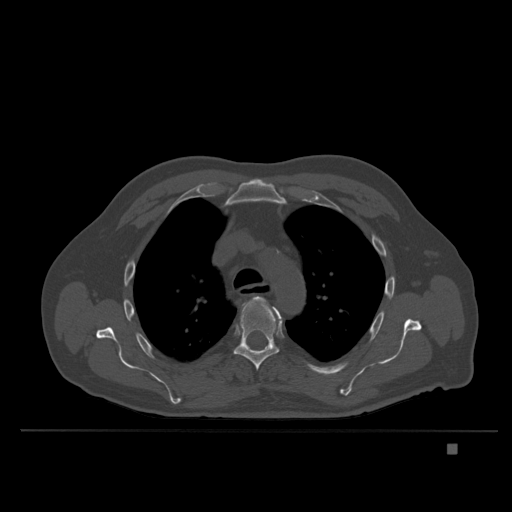
CT including the spine, one axial slice. Bone window (W 1800 / L 400 HU). 1.5 mm slice thickness. 512 × 512 image matrix, field of view 434 × 434 mm. Patient: male, 73 years. From the clinical record (not read from this slice): primary cancer: skin.
Outlined on this slice (semi-automatically segmented with operator editing):
- T4 vertebra: bounding box [x1, y1, x2, y2] px = [254, 297, 264, 301]
- T5 vertebra: [233, 297, 282, 371]